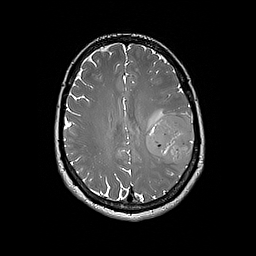
Brain MRI from a brain-tumour surgery series, one axial slice. Position 77 of 192 along the scan axis. 1 mm slice thickness. 256 × 256 image matrix. Case-level facts recorded for this patient, not image findings: histopathology: Glioblastoma; WHO grade: 4; IDH mutation: no; tumour location: Left Frontal.
Outlined on this slice (manually delineated by an expert):
- tumour: bounding box (x1, y1, x2, y2) in pixels: (146, 113, 195, 164)